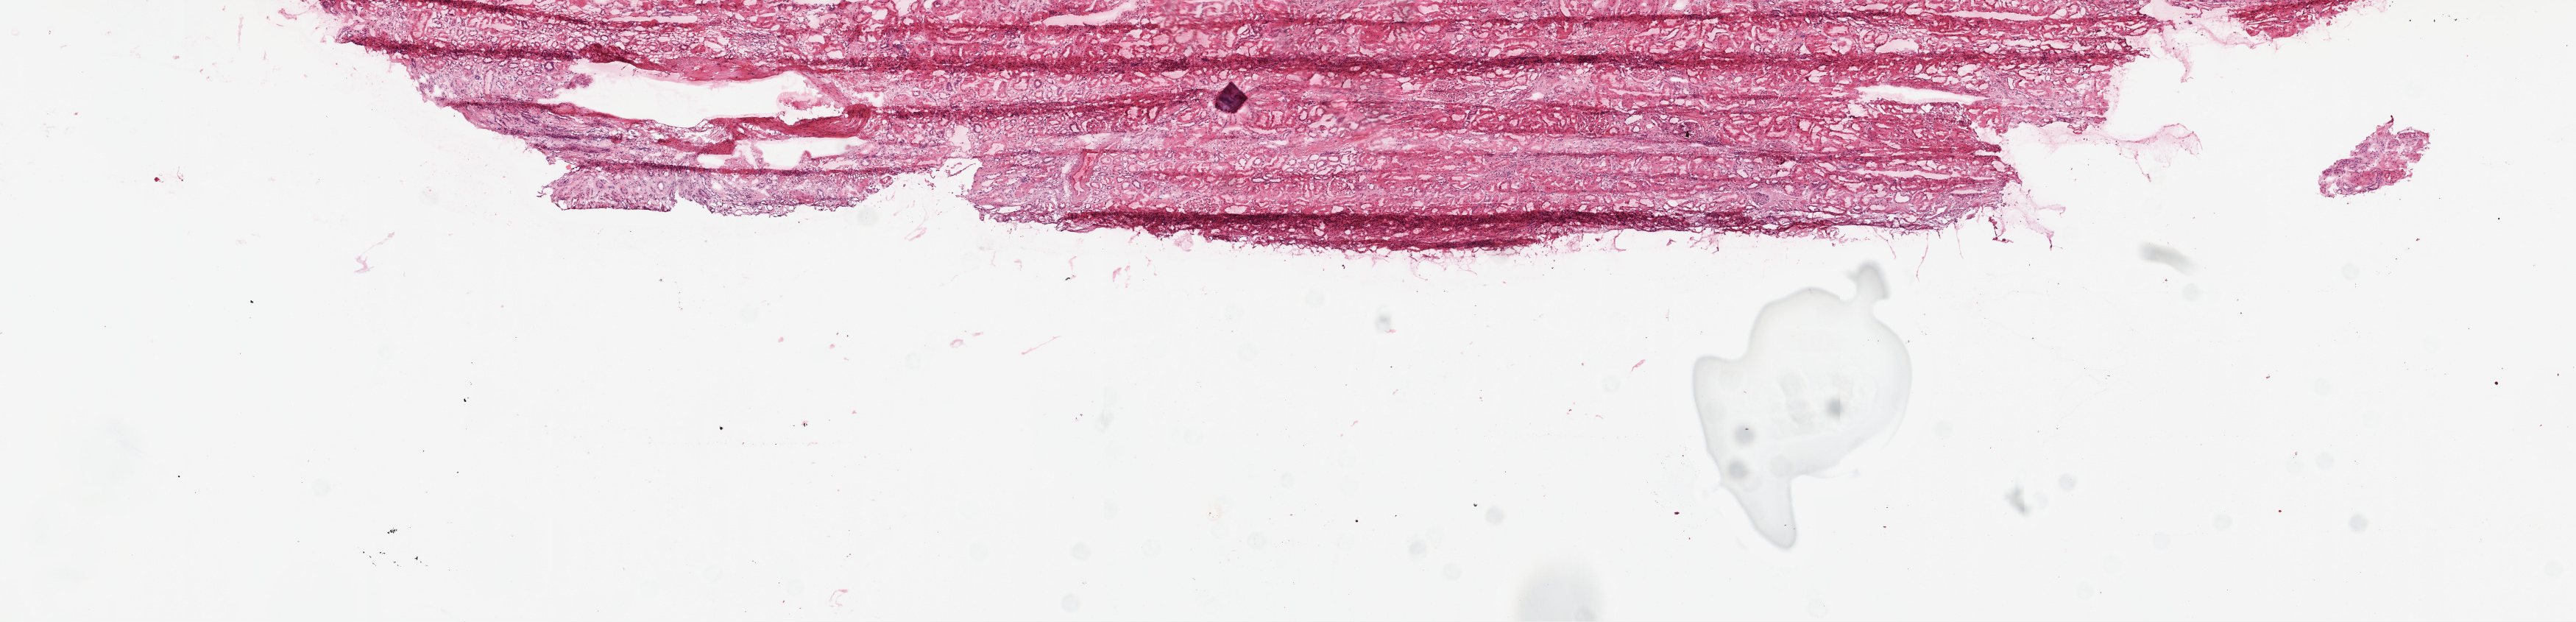
Digitized H&E tissue section (whole slide) — a low-resolution overview of the entire scanned area, about 14.0 x 3.4 mm, frozen section from the top of the tissue portion, sample: solid tissue normal (non-tumour tissue), kidney. Male patient; age at initial diagnosis 63 years.
This section: solid tissue normal (non-tumour) sample from the same patient. Patient diagnosis: Clear cell adenocarcinoma, NOS.